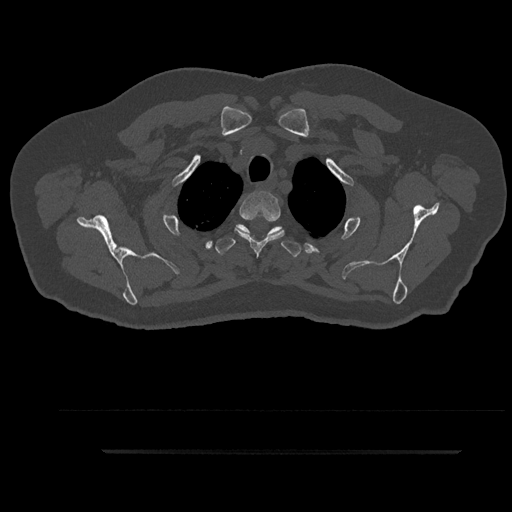
CT including the spine, one axial slice; slice 745 of 797 in the series (ordered by position); 120 kVp; bone window (W 1800 / L 400 HU); 0.5 mm slice thickness; 512 × 512 image matrix, field of view 432 × 432 mm. Male patient, age 63 years. Case-level facts recorded for this patient, not image findings: primary cancer: renal; vertebrae with lytic lesions (as recorded): T8.
Outlined on this slice (semi-automatically segmented with operator editing):
- T2 vertebra: bounding box [x1, y1, x2, y2] px = [235, 191, 285, 256]
- T3 vertebra: [215, 224, 302, 257]